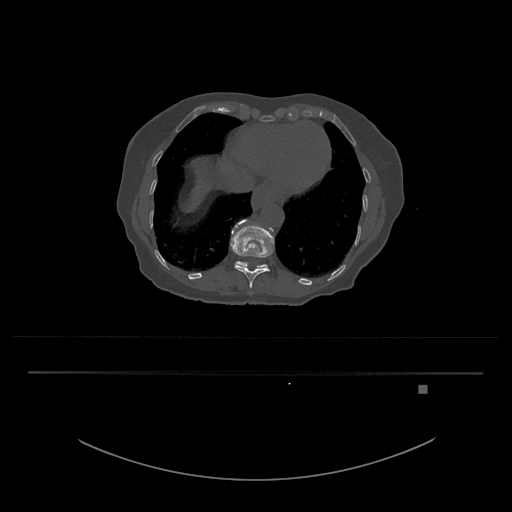
CT including the spine, one axial slice. Reconstruction kernel Br40s/3. Bone window (W 1800 / L 400 HU). 512 × 512 image matrix, field of view 500 × 500 mm. Patient: female, 57 years. Case-level facts recorded for this patient, not image findings: primary cancer: cervical.
Outlined on this slice (semi-automatic segmentation, software-assisted and operator-edited):
- T11 vertebra: bounding box [x1, y1, x2, y2] px = [230, 219, 275, 289]
- T12 vertebra: [235, 261, 268, 269]